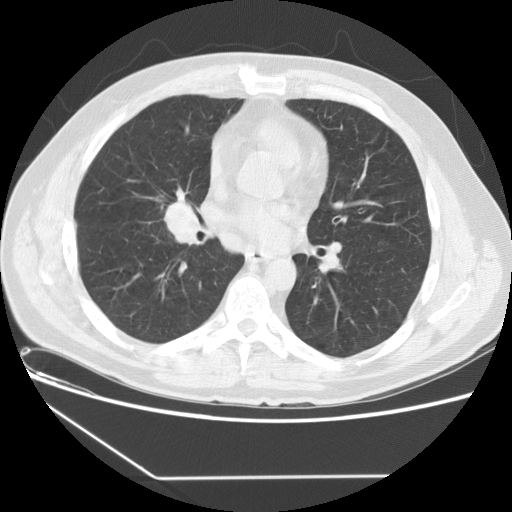
Low-dose screening chest CT, one axial slice; slice 75 of 154 in the series (ordered by position); 120 kVp; lung window (W 1500 / L -600 HU); 512 × 512 image matrix, field of view 370 × 370 mm.
Structures marked on this image (expert manual segmentation):
- lesion 1 (tumor, middle lobe of right lung): bounding box [x1, y1, x2, y2] px = [166, 203, 198, 243]